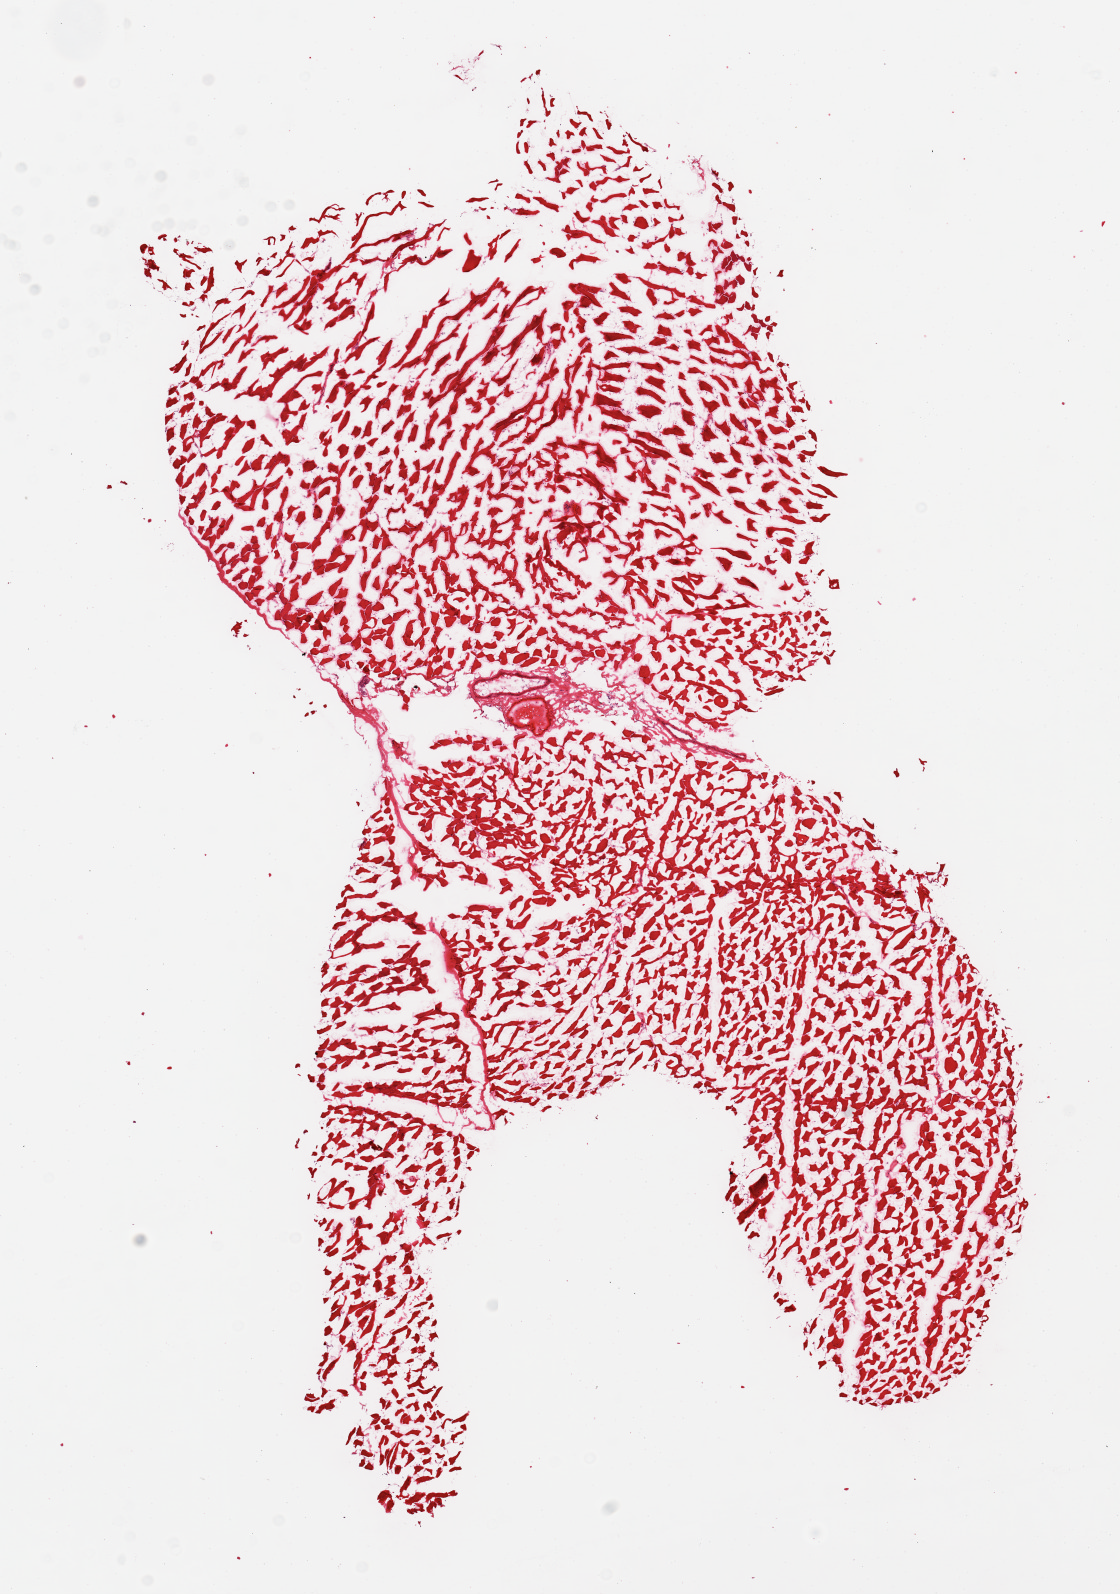
Digitized H&E-stained section, low-resolution overview of the scanned area, about 8.9 x 12.6 mm (slide scanned at 20x). Frozen section. Section of skeletal muscle (target tissue). Tissue donor sample.
Pathologist's review note for this sample: 1 piece.